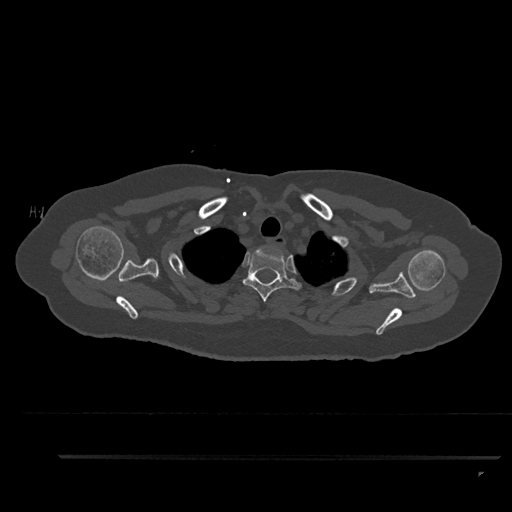
CT including the spine, one axial slice. Position 726 of 797 along the scan axis. 120 kVp. Bone window (W 1800 / L 400 HU). 0.5 mm slice thickness. 512 × 512 image matrix, field of view 408 × 408 mm. Patient: female, 44 years. Case-level facts recorded for this patient, not image findings: primary cancer: renal.
Structures marked on this image (semi-automatic segmentation, software-assisted and operator-edited):
- T1 vertebra: bounding box (x1, y1, x2, y2) in pixels: (276, 249, 278, 251)
- T2 vertebra: (242, 248, 302, 302)